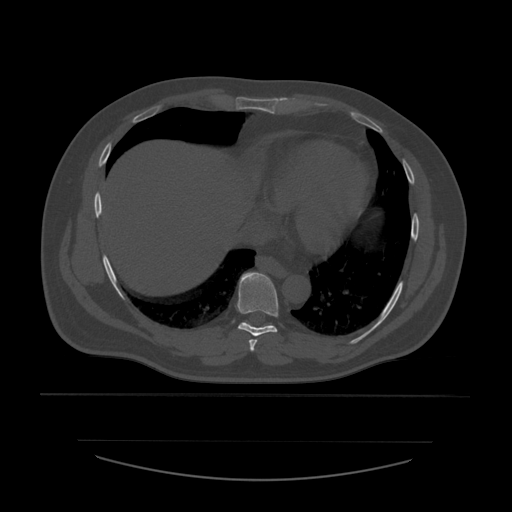
CT including the spine, one axial slice; slice 335 of 532 in the series (ordered by position); 120 kVp; bone window (W 1800 / L 400 HU); 1.25 mm slice thickness; 512 × 512 image matrix, field of view 441 × 441 mm. Patient age 44 years. From the clinical record (not read from this slice): primary cancer: soft tissue sarcoma.
Annotated regions visible in this slice (semi-automatic segmentation, software-assisted and operator-edited):
- T7 vertebra: box from (x=249, y=340) to (x=258, y=353) px
- T8 vertebra: (x=237, y=272)–(x=279, y=337)